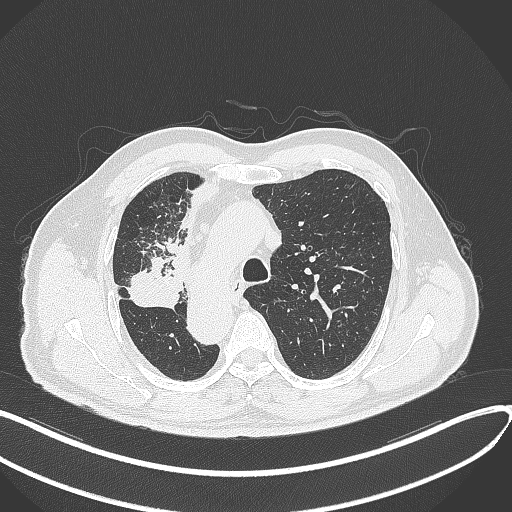
Chest CT, one axial slice; position 227 of 300 along the scan axis; lung window (W 1500 / L -600 HU); 1 mm slice thickness; 512 × 512 image matrix. Male patient, age 67 years. From the clinical record (not read from this slice): clinical TNM (as recorded): T2a N0 M0.
Annotated regions visible in this slice (rectangle marked by the reading radiologist):
- lung tumour (recorded histology: squamous cell carcinoma): box from (x=125, y=257) to (x=184, y=312) px